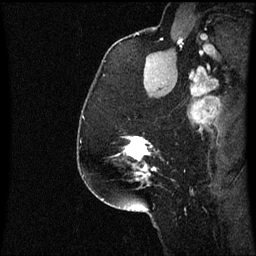
Breast MRI (dynamic contrast-enhanced), one sagittal slice. Slice 46 of 60 in the series (ordered by position). Dynamic contrast-enhanced series, image 2 of 3 at this slice position (ordered by acquisition). 1.5 T. TE 4.2 ms, TR 8.9 ms. 256 × 256 image matrix, field of view 200 × 200 mm. Patient: female, 58 years. From the clinical record (not read from this slice): setting: breast cancer imaged before/during neoadjuvant chemotherapy; receptor status: triple-negative.
Structures marked on this image (semi-automatically segmented with operator editing):
- analysis volume of interest (the breast-tissue region the enhancement analysis was run in; not a lesion): bounding box <124,136,157,179> (left, top, right, bottom; pixels)
- tumour enhancement mask (voxels above the 70 % enhancement threshold inside the analysis volume of interest): <126,136,157,177>